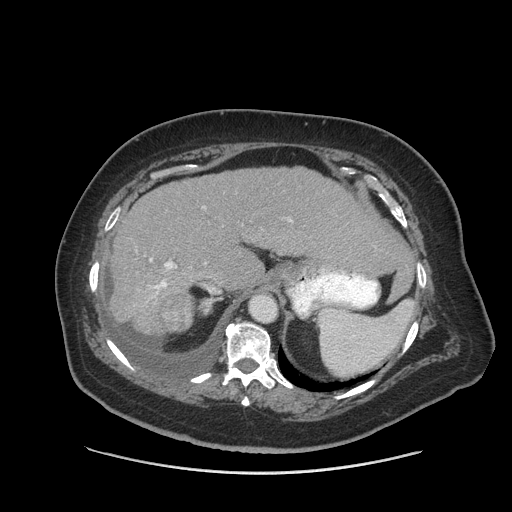
Contrast-enhanced abdominal CT (liver protocol), one axial slice. Reconstruction kernel STANDARD. 140 kVp. Soft-tissue window (W 400 / L 40 HU). 512 × 512 image matrix. From the clinical record (not read from this slice): diagnosis: hepatocellular carcinoma (patient treated with transarterial chemoembolisation; whether this scan precedes or follows treatment is not stated here); TNM stage (as recorded): Stage-I; Child-Pugh class: A; tumour differentiation: well differentiated.
Annotated regions visible in this slice (semi-automatically segmented with operator editing):
- liver parenchyma outside the tumour (the mass and vessels are separate outlines, so this box may not span the whole liver): bounding box <110,166,404,334> (left, top, right, bottom; pixels)
- mass: <160,289,193,333>
- liver vessels: <150,220,291,294>